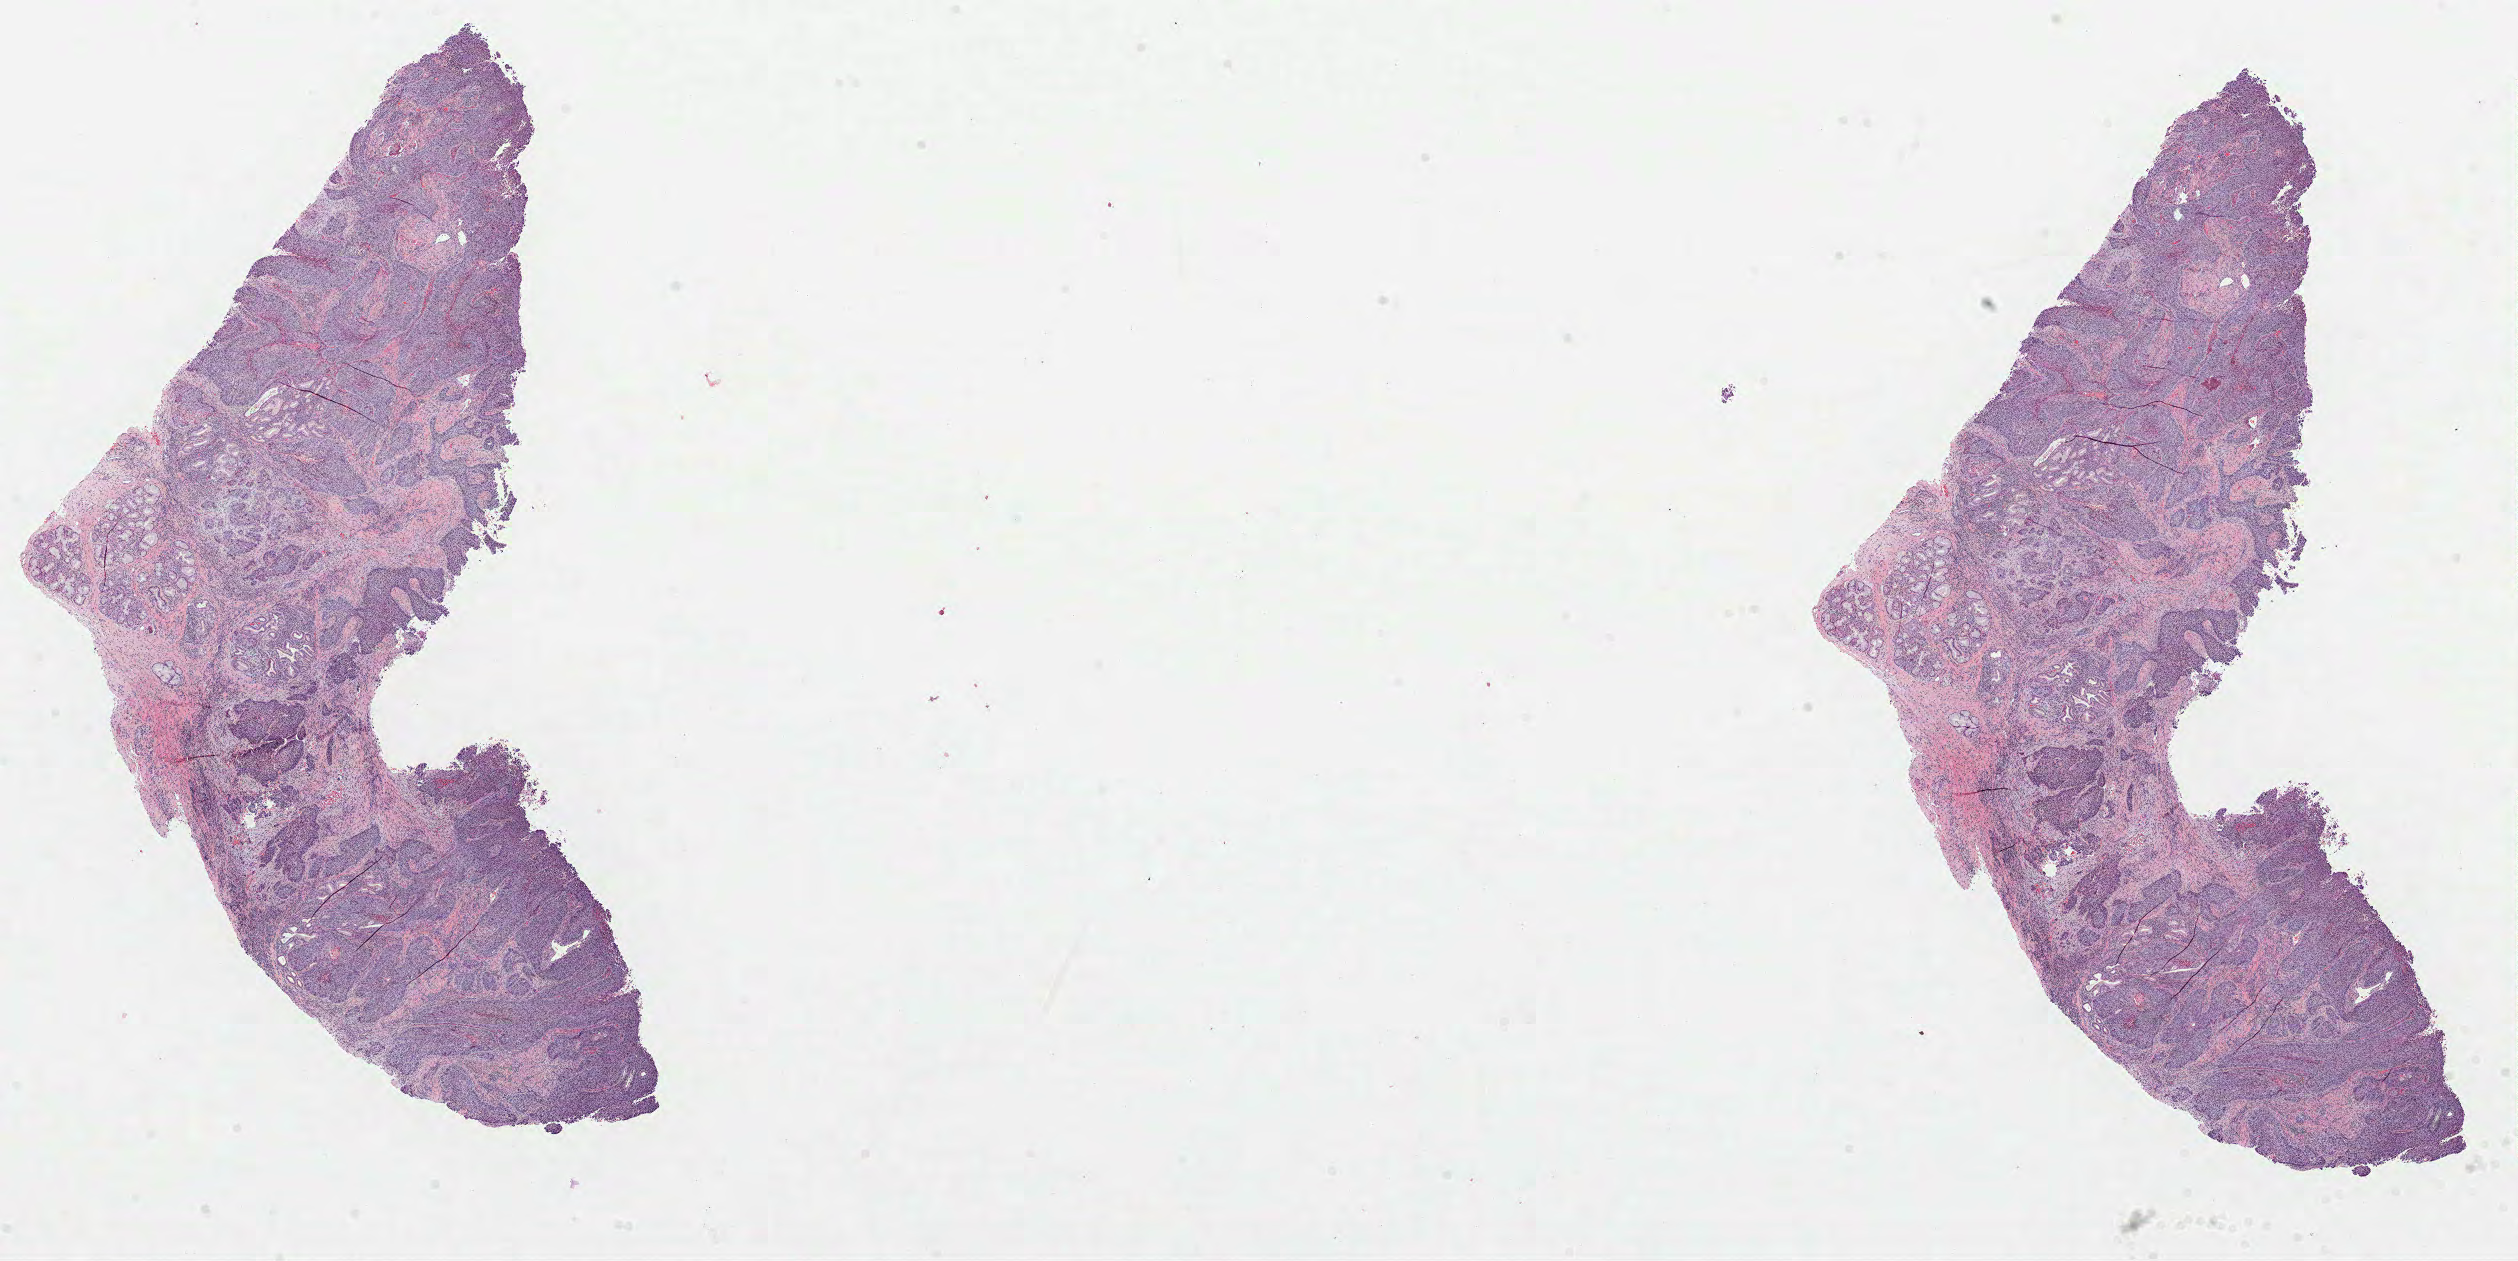
Hematoxylin and eosin (H&E) stained whole-slide image, a low-resolution overview of the entire scanned area, about 20.3 x 10.2 mm (from a 40x scan); formalin-fixed paraffin-embedded (FFPE) diagnostic section; head and neck, primary tumour sample. Male, age 53 years at initial diagnosis. Histologic grade: G2 (moderately differentiated).
- histologic diagnosis: Squamous cell carcinoma, NOS (larynx, NOS)
- TNM: T4a N2c
- AJCC pathologic stage: IVA